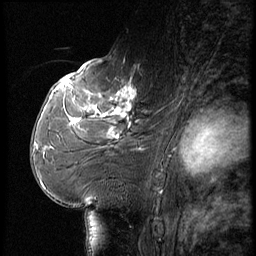
Breast MRI (dynamic contrast-enhanced), one sagittal slice. Position 34 of 56 along the scan axis. Dynamic contrast-enhanced series, image 2 of 3 at this slice position (ordered by acquisition). 1.5 T. TE 4.2 ms, TR 9 ms. 2.5 mm slice thickness. 256 × 256 image matrix, field of view 180 × 180 mm. Female patient, age 61 years. Case-level facts recorded for this patient, not image findings: setting: breast cancer imaged before/during neoadjuvant chemotherapy; receptor status: HR-positive, HER2-negative.
Outlined on this slice (semi-automatic segmentation, software-assisted and operator-edited):
- analysis volume of interest (the breast-tissue region the enhancement analysis was run in; not a lesion): bounding box [x1, y1, x2, y2] px = [65, 74, 150, 175]
- tumour enhancement mask (voxels above the 140 % enhancement threshold inside the analysis volume of interest): [70, 86, 136, 139]